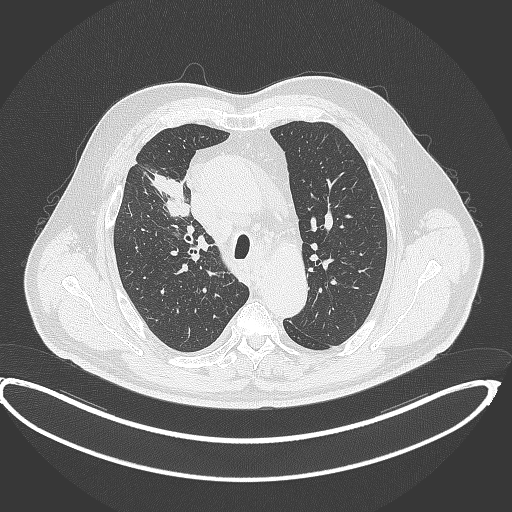
Chest CT, one axial slice; position 290 of 390 along the scan axis; 120 kVp; lung window (W 1500 / L -600 HU); 512 × 512 image matrix. Male patient, age 62 years. From the clinical record (not read from this slice): clinical TNM (as recorded): T1c N3 M1c.
Annotated regions visible in this slice (rectangle marked by the reading radiologist):
- lung tumour (recorded histology: adenocarcinoma): bounding box [x1, y1, x2, y2] px = [146, 167, 191, 220]